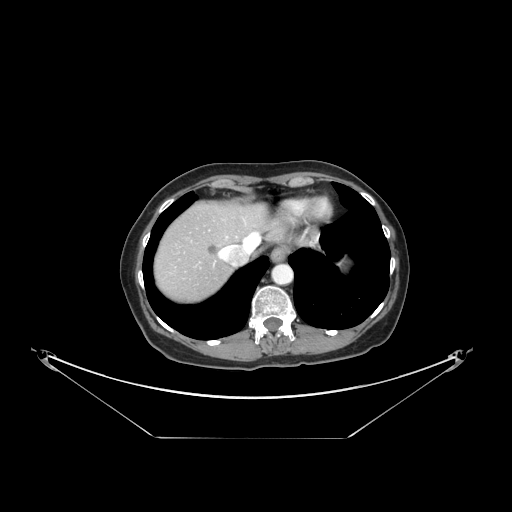
Contrast-enhanced abdominal CT, one axial slice; position 129 of 148 along the scan axis; reconstruction kernel STANDARD; intravenous contrast given; soft-tissue window (W 400 / L 40 HU); 512 × 512 image matrix, field of view 500 × 500 mm. Female patient, age 73 years. Case-level facts recorded for this patient, not image findings: diagnosis: colorectal cancer liver metastases, imaged before liver resection; multiple liver metastases: no; largest metastasis: 1 cm.
Outlined on this slice (outlined manually by an expert reader):
- liver: bounding box <155,203,265,303> (left, top, right, bottom; pixels)
- planned liver remnant (the part of the liver to remain after resection): <183,203,265,245>
- liver metastasis: <207,244,218,256>